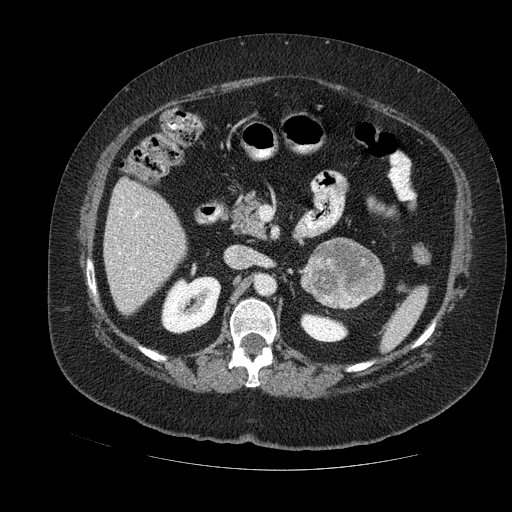
Contrast-enhanced abdominal CT, one axial slice; slice 65 of 121 in the series (ordered by position); soft-tissue window (W 400 / L 40 HU); 512 × 512 image matrix. Female patient. From the clinical record (not read from this slice): diagnosis: adrenocortical carcinoma; tumour side: left adrenal; tumour size at pathology: 8 cm; Ki-67 index: 7 %; stage (as recorded): 2.
Outlined on this slice (semi-automatically segmented with operator editing):
- mass: bounding box <304,239,379,306> (left, top, right, bottom; pixels)